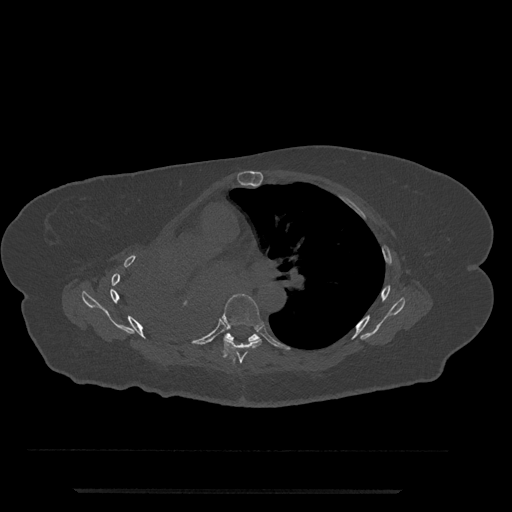
CT including the spine, one axial slice; position 478 of 797 along the scan axis; 120 kVp; bone window (W 1800 / L 400 HU); 0.5 mm slice thickness; 512 × 512 image matrix, field of view 440 × 440 mm. Patient: female, 51 years. From the clinical record (not read from this slice): primary cancer: neuro.
Structures marked on this image (semi-automatically segmented with operator editing):
- T6 vertebra: bounding box (x1, y1, x2, y2) in pixels: (219, 294, 262, 364)
- T7 vertebra: (225, 333, 260, 341)